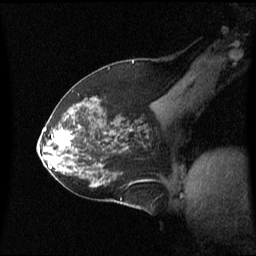
Breast MRI (dynamic contrast-enhanced), one sagittal slice. Slice 35 of 60 in the series (ordered by position). Dynamic contrast-enhanced series, image 2 of 3 at this slice position (ordered by acquisition). 1.5 T. TE 4.2 ms, TR 8.4 ms. 2 mm slice thickness. 256 × 256 image matrix, field of view 240 × 240 mm. Female patient, age 59 years. Case-level facts recorded for this patient, not image findings: setting: breast cancer imaged before/during neoadjuvant chemotherapy; receptor status: HR-positive, HER2-negative.
Structures marked on this image (semi-automatically segmented with operator editing):
- analysis volume of interest (the breast-tissue region the enhancement analysis was run in; not a lesion): bounding box (x1, y1, x2, y2) in pixels: (46, 114, 86, 163)
- tumour enhancement mask (voxels above the 70 % enhancement threshold inside the analysis volume of interest): (55, 132, 72, 147)